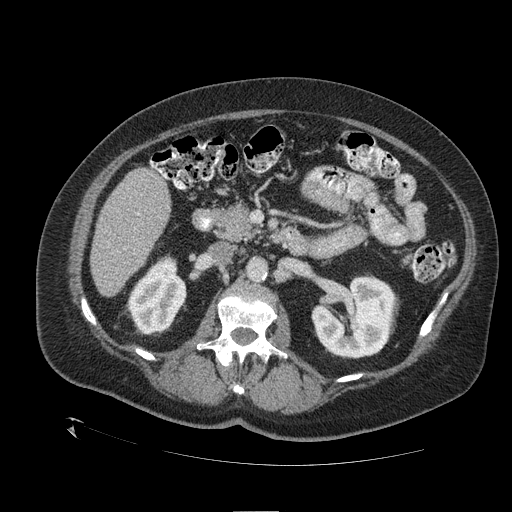
Contrast-enhanced abdominal CT (liver protocol), one axial slice. Slice 49 of 109 in the series (ordered by position). Reconstruction kernel STANDARD. One of 2 acquisitions stored at this slice position. Soft-tissue window (W 400 / L 40 HU). 512 × 512 image matrix, field of view 460 × 460 mm. From the clinical record (not read from this slice): diagnosis: hepatocellular carcinoma (patient treated with transarterial chemoembolisation; whether this scan precedes or follows treatment is not stated here); TNM stage (as recorded): Stage-I; Child-Pugh class: A.
Structures marked on this image (semi-automatic segmentation, software-assisted and operator-edited):
- liver parenchyma outside the tumour (the mass and vessels are separate outlines, so this box may not span the whole liver): bounding box [x1, y1, x2, y2] px = [90, 168, 170, 296]
- liver vessels: [137, 213, 140, 215]